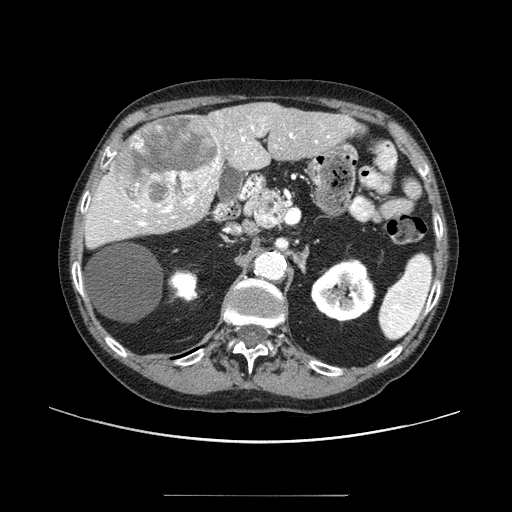
Contrast-enhanced abdominal CT (liver protocol), one axial slice; position 48 of 91 along the scan axis; reconstruction kernel STANDARD; one of 2 acquisitions stored at this slice position; soft-tissue window (W 400 / L 40 HU); 2.5 mm slice thickness; 512 × 512 image matrix, field of view 400 × 400 mm. Case-level facts recorded for this patient, not image findings: diagnosis: hepatocellular carcinoma (patient treated with transarterial chemoembolisation; whether this scan precedes or follows treatment is not stated here); TNM stage (as recorded): Stage-I; Child-Pugh class: A; tumour differentiation: moderately differentiated.
Annotated regions visible in this slice (semi-automatically segmented with operator editing):
- liver parenchyma outside the tumour (the mass and vessels are separate outlines, so this box may not span the whole liver): bounding box (x1, y1, x2, y2) in pixels: (88, 102, 364, 236)
- mass: (112, 115, 220, 211)
- liver vessels: (98, 117, 330, 227)